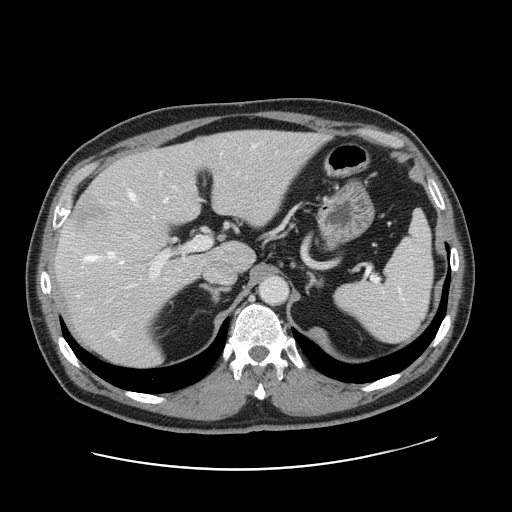
Contrast-enhanced abdominal CT, one axial slice; position 108 of 178 along the scan axis; soft-tissue window (W 400 / L 40 HU); 512 × 512 image matrix. Male patient, age 63 years. From the clinical record (not read from this slice): diagnosis: colorectal cancer liver metastases, imaged before liver resection; multiple liver metastases: yes; largest metastasis: 8 cm.
Outlined on this slice (expert manual segmentation):
- hepatic veins: box from (x=86, y=146) to (x=255, y=264) px
- liver: (x=56, y=130)–(x=321, y=368)
- planned liver remnant (the part of the liver to remain after resection): (x=128, y=130)–(x=321, y=271)
- portal vein (with intrahepatic branches): (x=151, y=199)–(x=212, y=276)
- liver metastasis: (x=71, y=207)–(x=103, y=229)